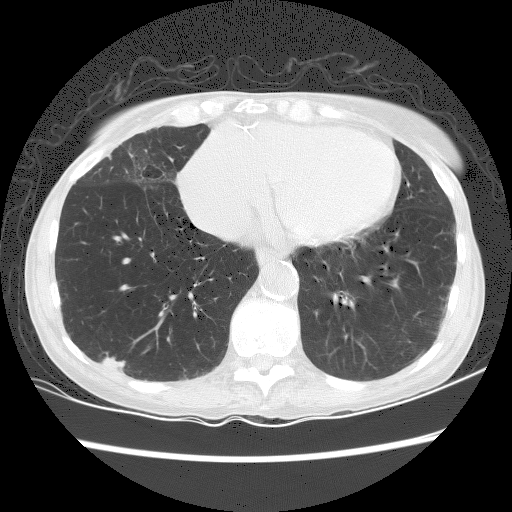
Axial slice from a low-dose chest CT screening exam. Baseline screening round. Lung window (W 1500 / L -600 HU). Female, age 70 years at enrolment. Current smoker at enrolment.
Expert-annotated lung lesion, box from (x=89, y=345) to (x=140, y=385) px. The screening reader recorded 2 non-calcified nodules or masses ≥4 mm on this exam; which of them this box marks is not recorded. Official screen result: positive, change unspecified: nodule(s) >= 4 mm or enlarging nodule(s), mass(es), or other non-specific abnormalities suspicious for lung cancer. Lung cancer was diagnosed 125 days after this screen: squamous cell carcinoma, NOS, right lower lobe, well differentiated (G1), stage IA (AJCC 6th edition), 25 mm at pathology.